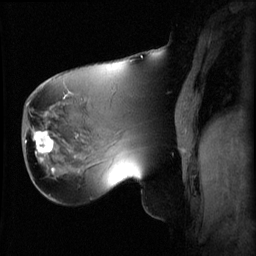
Breast MRI (dynamic contrast-enhanced), one sagittal slice. Slice 22 of 60 in the series (ordered by position). 3 images stored at this slice position (order not interpretable as contrast timing). 1.5 T. TE 4.2 ms, TR 8.2 ms. 2.2 mm slice thickness. 256 × 256 image matrix. Patient: female, 62 years.
Annotated regions visible in this slice (semi-automatic segmentation, software-assisted and operator-edited):
- analysis volume of interest (the breast-tissue region the enhancement analysis was run in; not a lesion): bounding box [x1, y1, x2, y2] px = [26, 126, 59, 165]
- tumour enhancement mask (voxels above the 70 % enhancement threshold inside the analysis volume of interest): [32, 130, 55, 161]